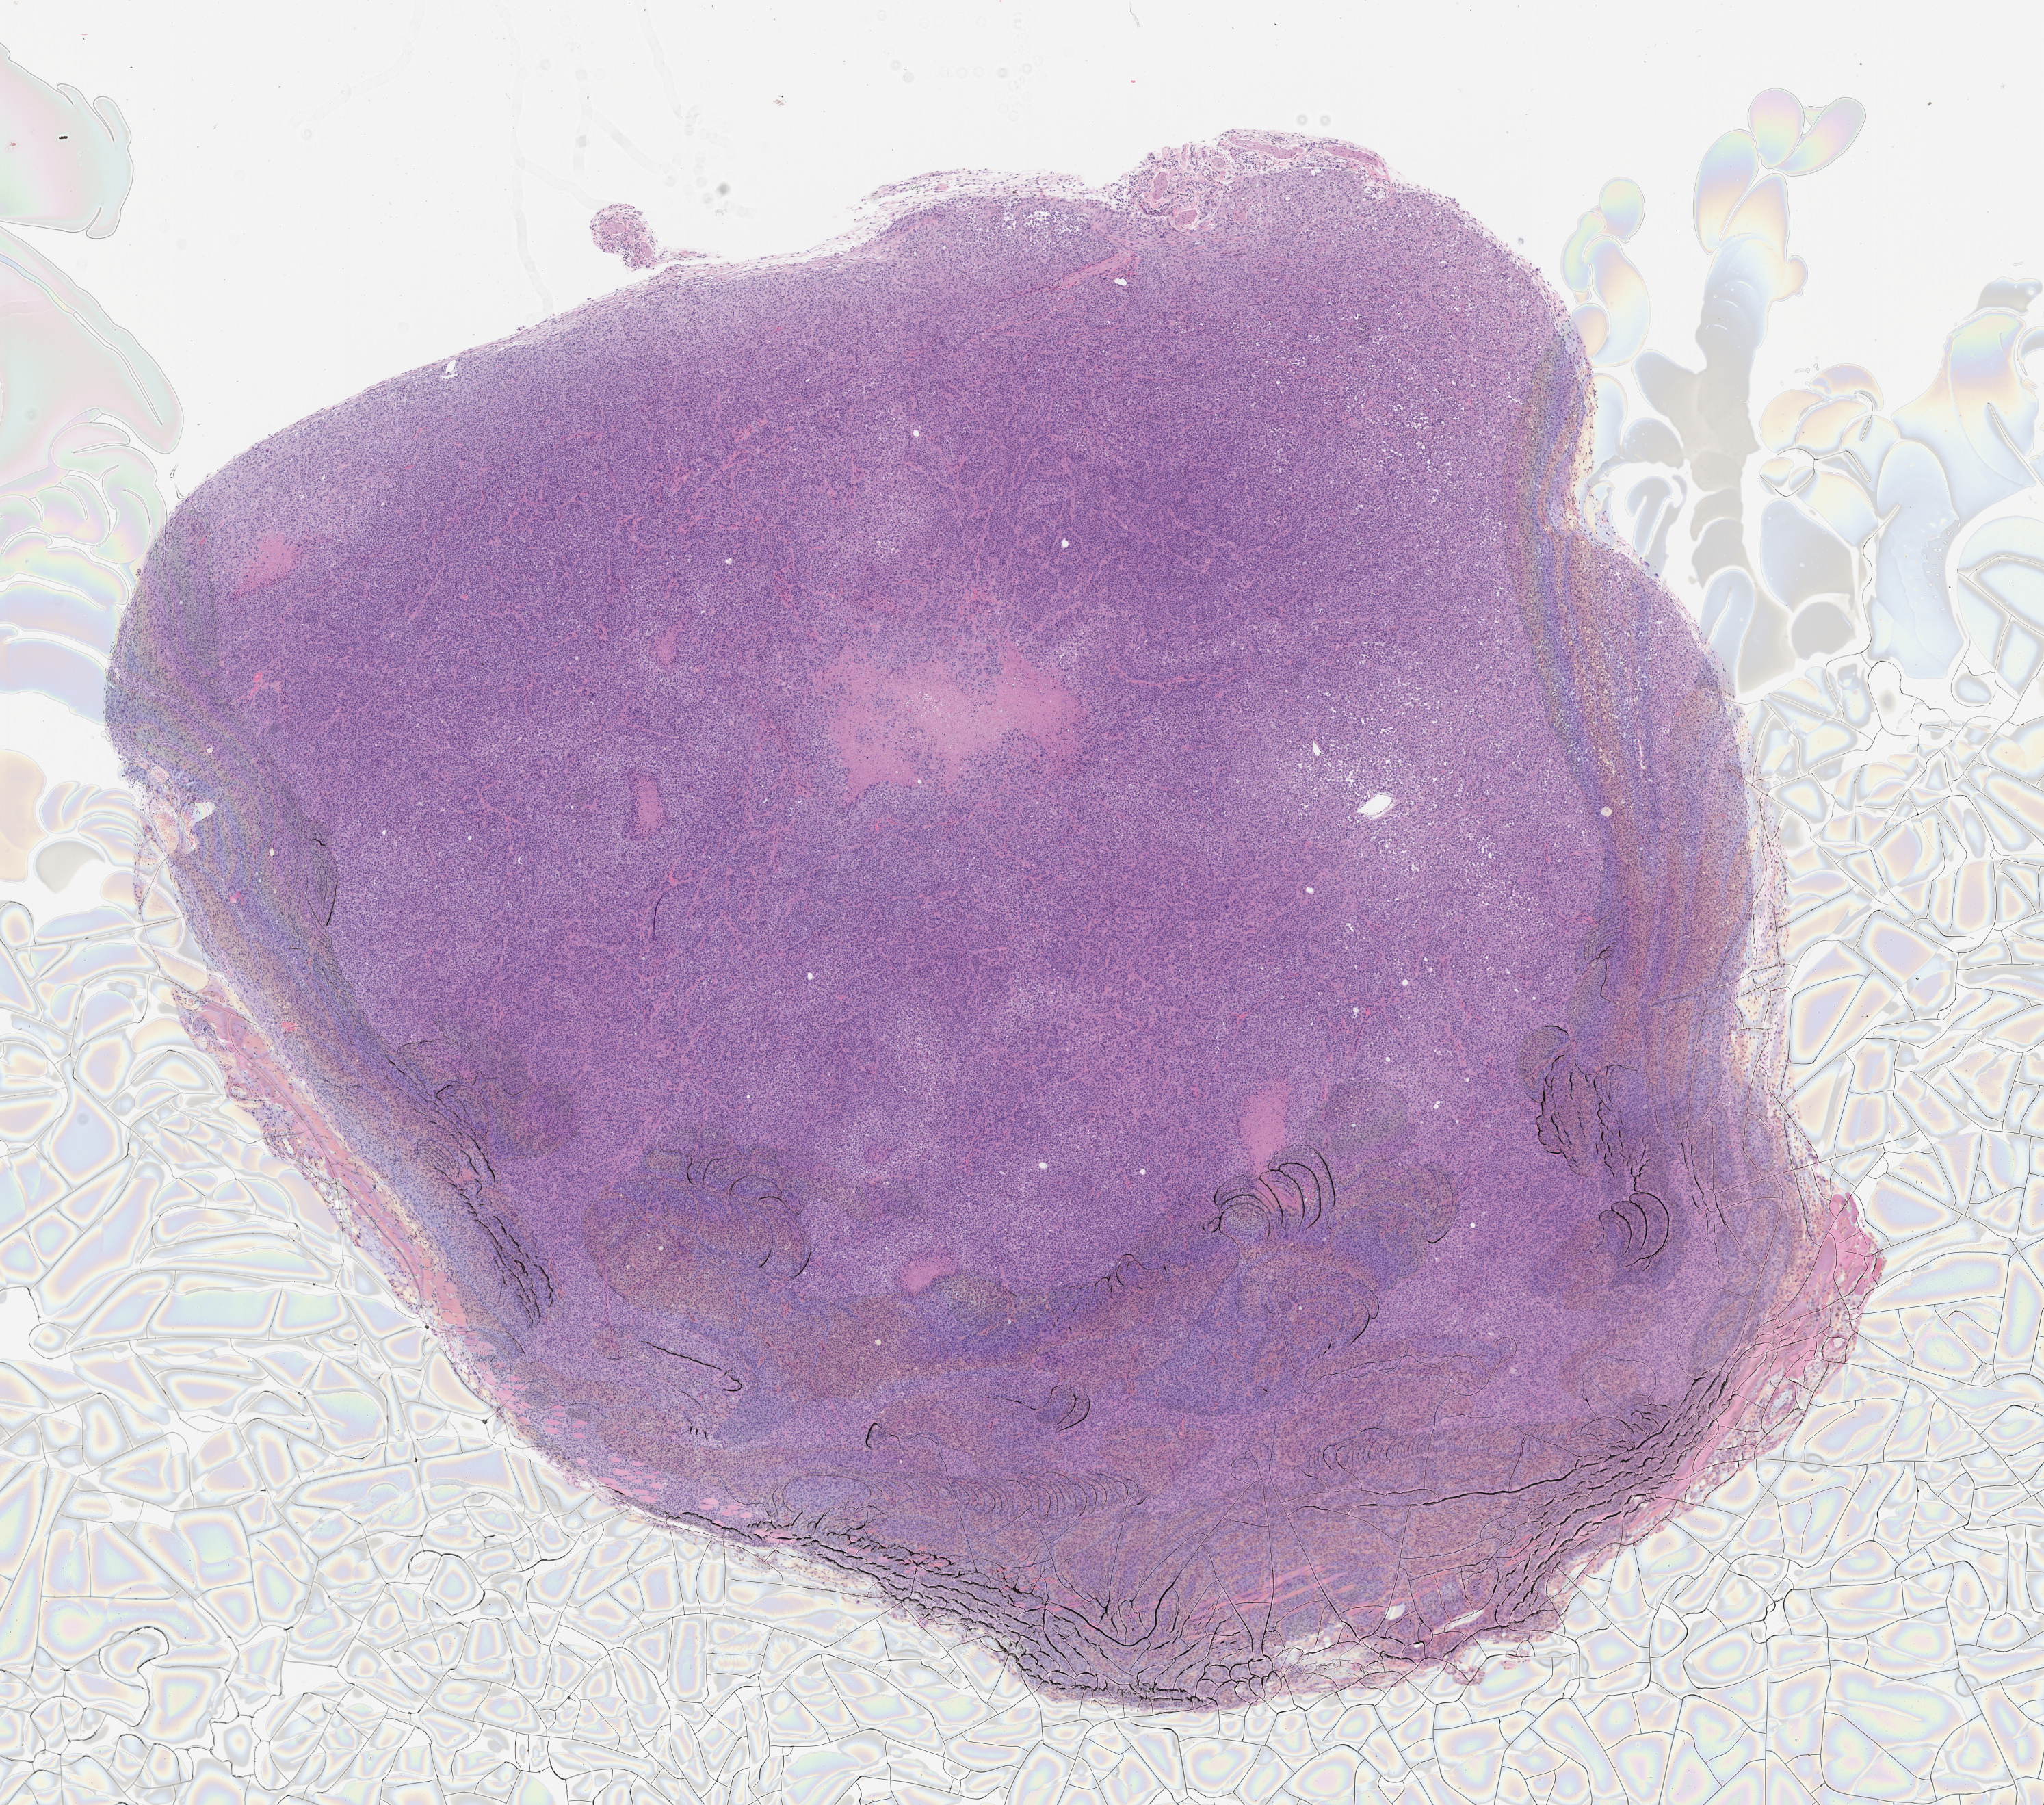
Haematoxylin and eosin whole-slide image of a patient-derived xenograft (PDX) tumor grown in a mouse, passage 0, low-resolution overview of the scanned area, about 12.0 x 10.6 mm; formalin-fixed, paraffin-embedded (FFPE) tissue.
* originating patient diagnosis: Mesothelial Neoplasm